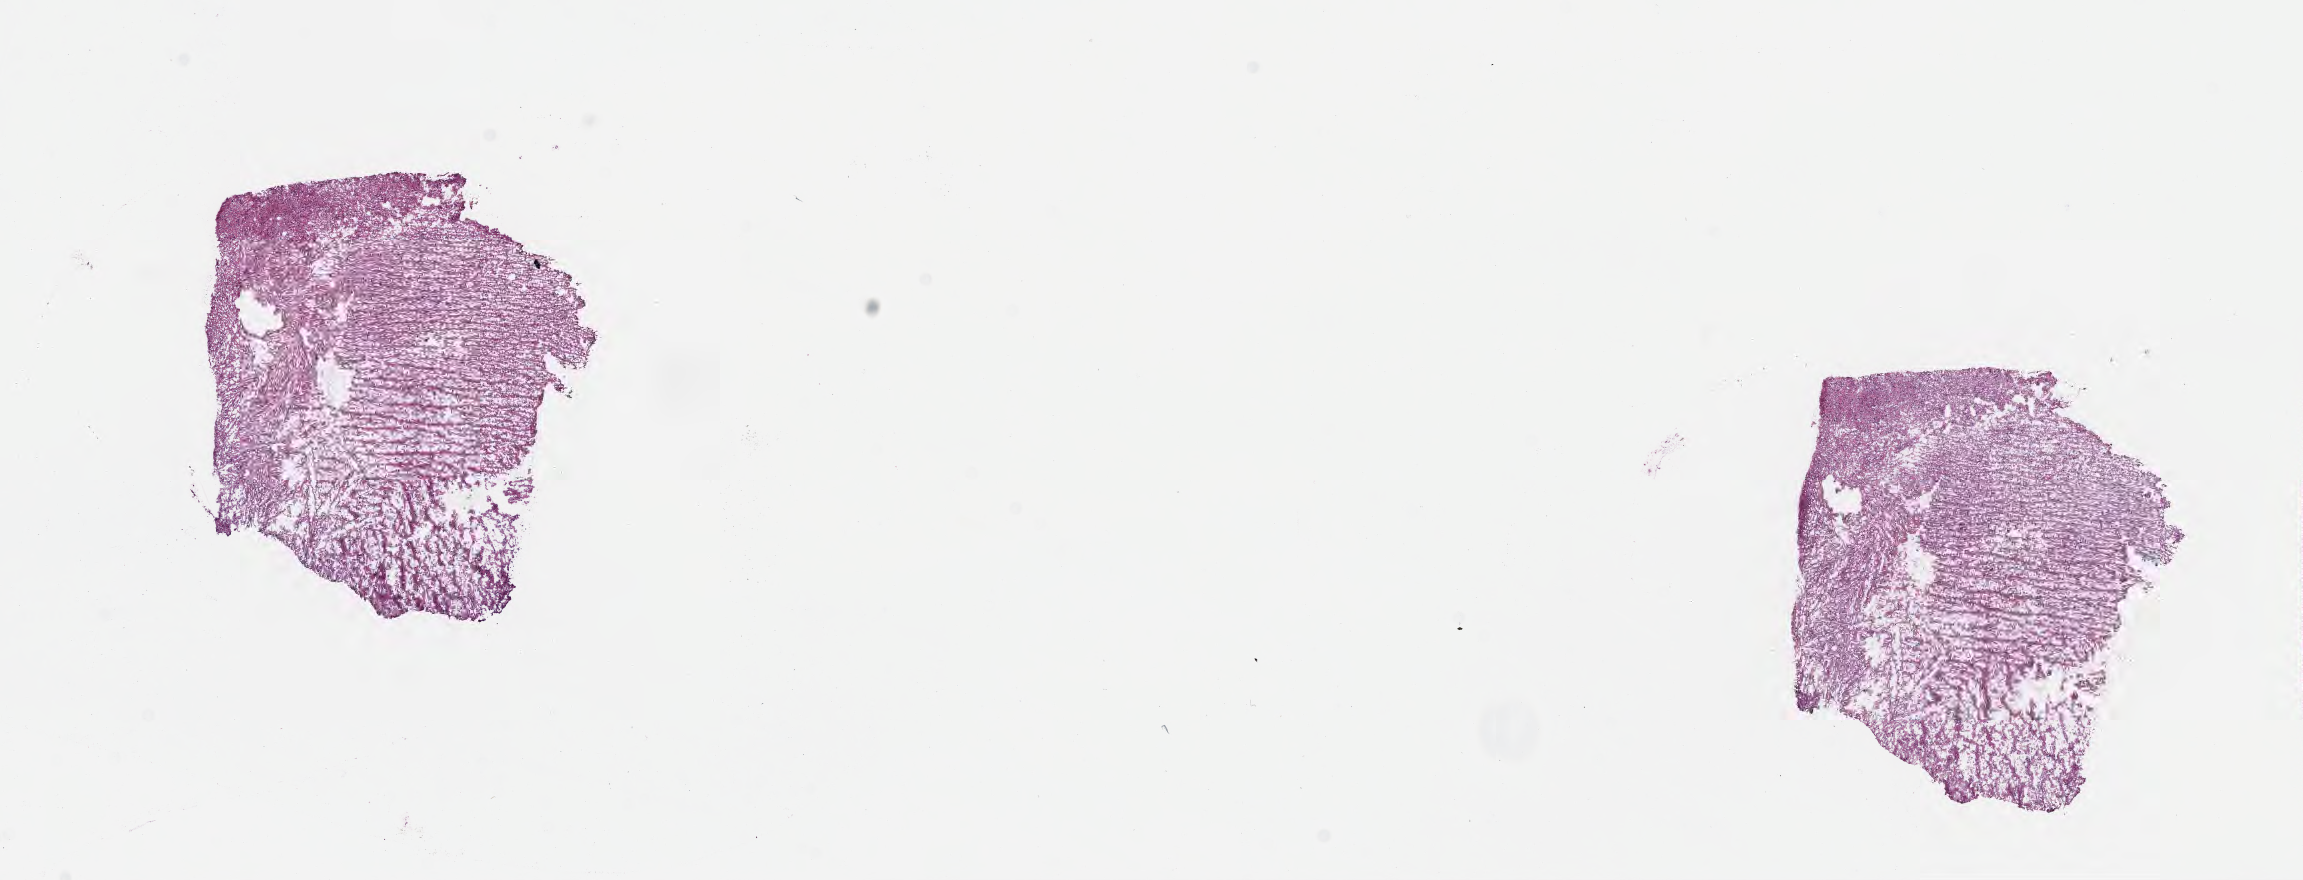
Digitized haematoxylin and eosin-stained section, whole scanned area (about 18.6 x 7.1 mm) shown as a low-resolution overview, frozen section (tissue freezing medium), specimen: recurrent tumor, anatomic site: brain. Female, age 59 years at initial diagnosis. Pathologist review of this section (percent, as recorded): tumor cells 80%, tumor nuclei 92%, stromal cells 13%, necrosis 0%, normal cells 7%. Infiltration values recorded for this section: lymphocyte infiltration 0%, monocyte infiltration 0%, neutrophil infiltration 0%.
Patient diagnosis: Glioblastoma, NOS. Section: bottom of the tissue portion.